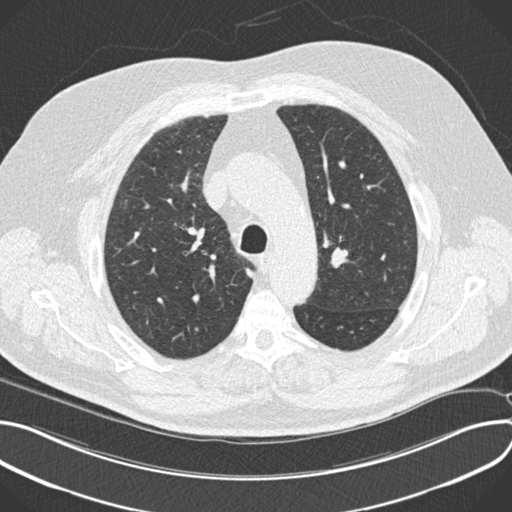
Chest CT (low-dose screening protocol), one axial image; third screening round (two years after baseline); lung window (W 1500 / L -600 HU); standard (soft-tissue) reconstruction kernel (B30f); 512 × 512 image matrix, field of view 380 × 380 mm. Male participant, aged 64 years at enrolment. Current smoker at enrolment.
Expert reader's lesion annotation, bounding box <107,188,144,225> (left, top, right, bottom; pixels). Screening reader's record for this exam (one nodule recorded; not confirmed to be the boxed lesion): non-calcified nodule or mass ≥4 mm, right upper lobe, 7 × 6 mm, smooth margins, soft tissue attenuation, pre-existing on the prior screen: no. Official screen result: positive, other. Participant outcome: lung cancer diagnosed 104 days after this screen — squamous cell carcinoma, NOS, right upper lobe, moderately differentiated (G2), stage IA (AJCC 6th edition), 7 mm at pathology.